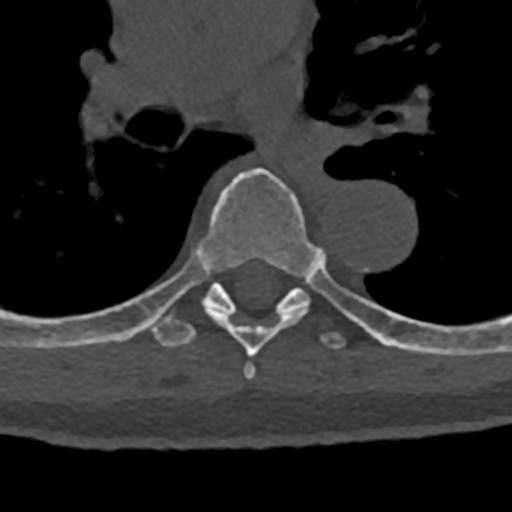
CT including the spine, one axial slice. 120 kVp. Bone window (W 1800 / L 400 HU). 512 × 512 image matrix. Patient: male, 74 years. Case-level facts recorded for this patient, not image findings: primary cancer: renal.
Structures marked on this image (semi-automatically segmented with operator editing):
- T6 vertebra: box from (x=144, y=167) to (x=318, y=380) px
- T7 vertebra: (x=70, y=247)–(x=432, y=354)